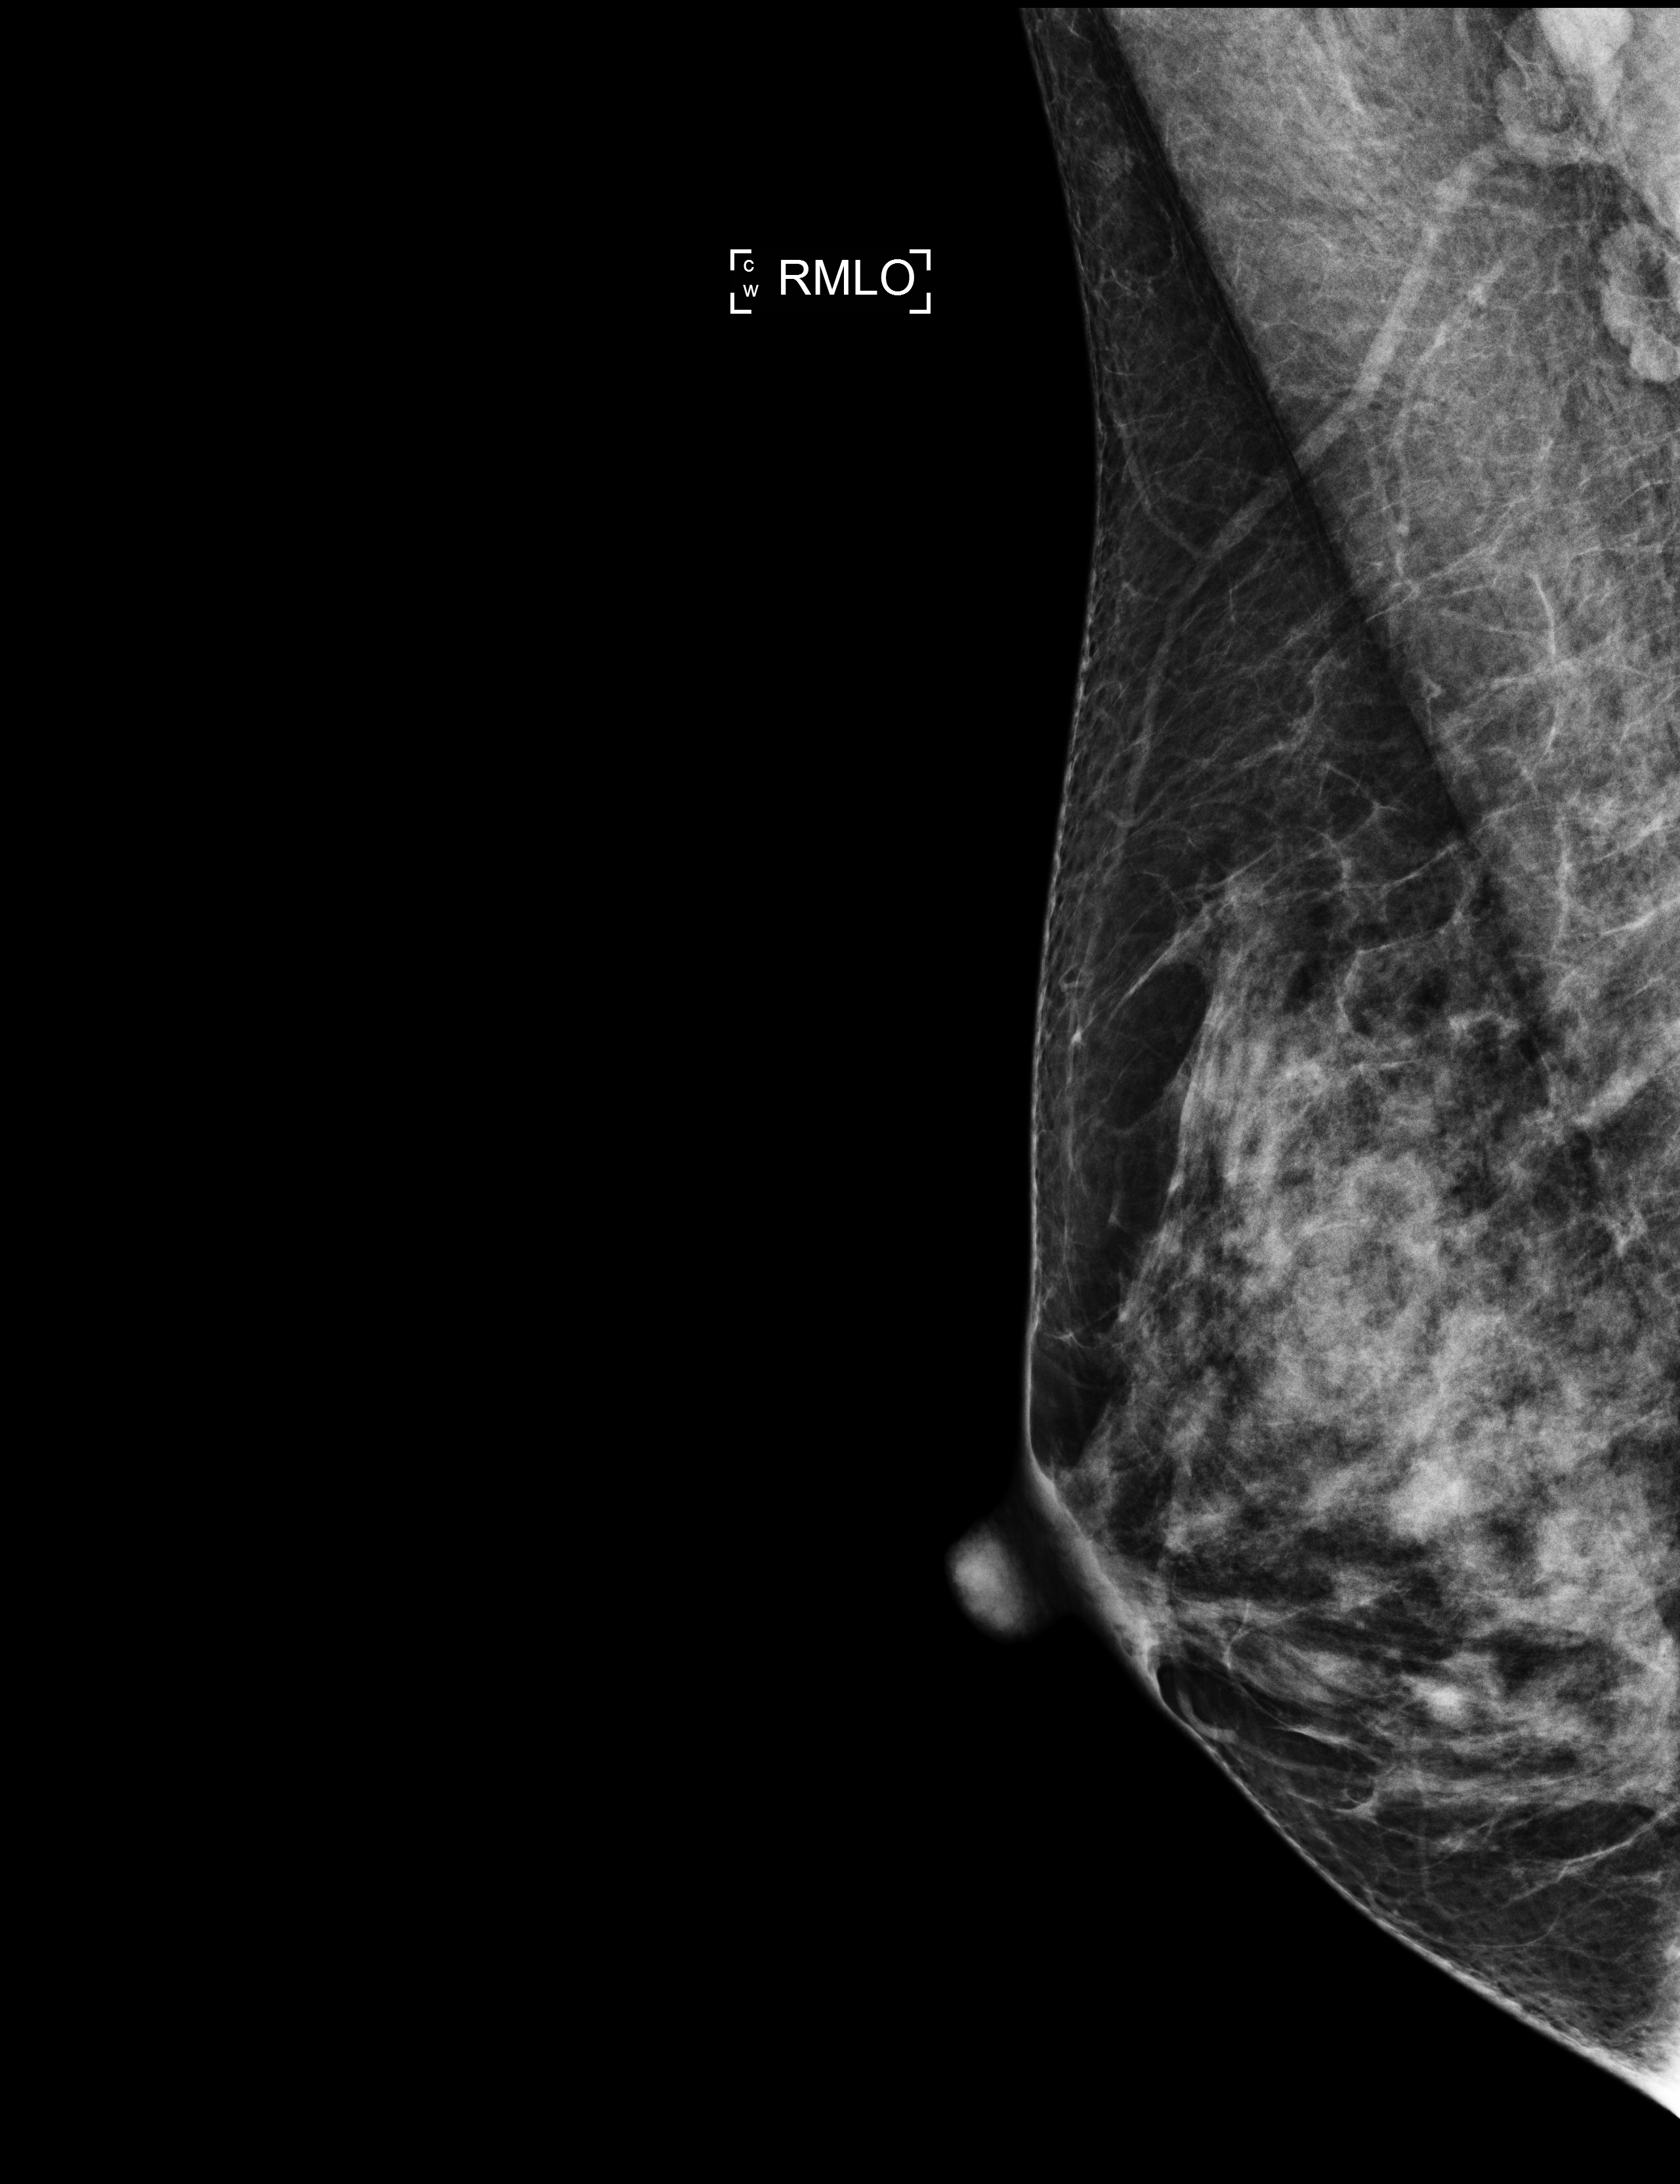
Annual screening mammography examination; system: Selenia Dimensions. Female patient, age 41 years.
Image type: full-field digital mammogram. Breast: right. Projection: medio-lateral oblique projection. Breast density at the screening exam (both breasts): extremely dense (BI-RADS density category d). Final BI-RADS assessment for this screening round (tomosynthesis exam, both breasts): category 1. Recall: no recall after this screen.